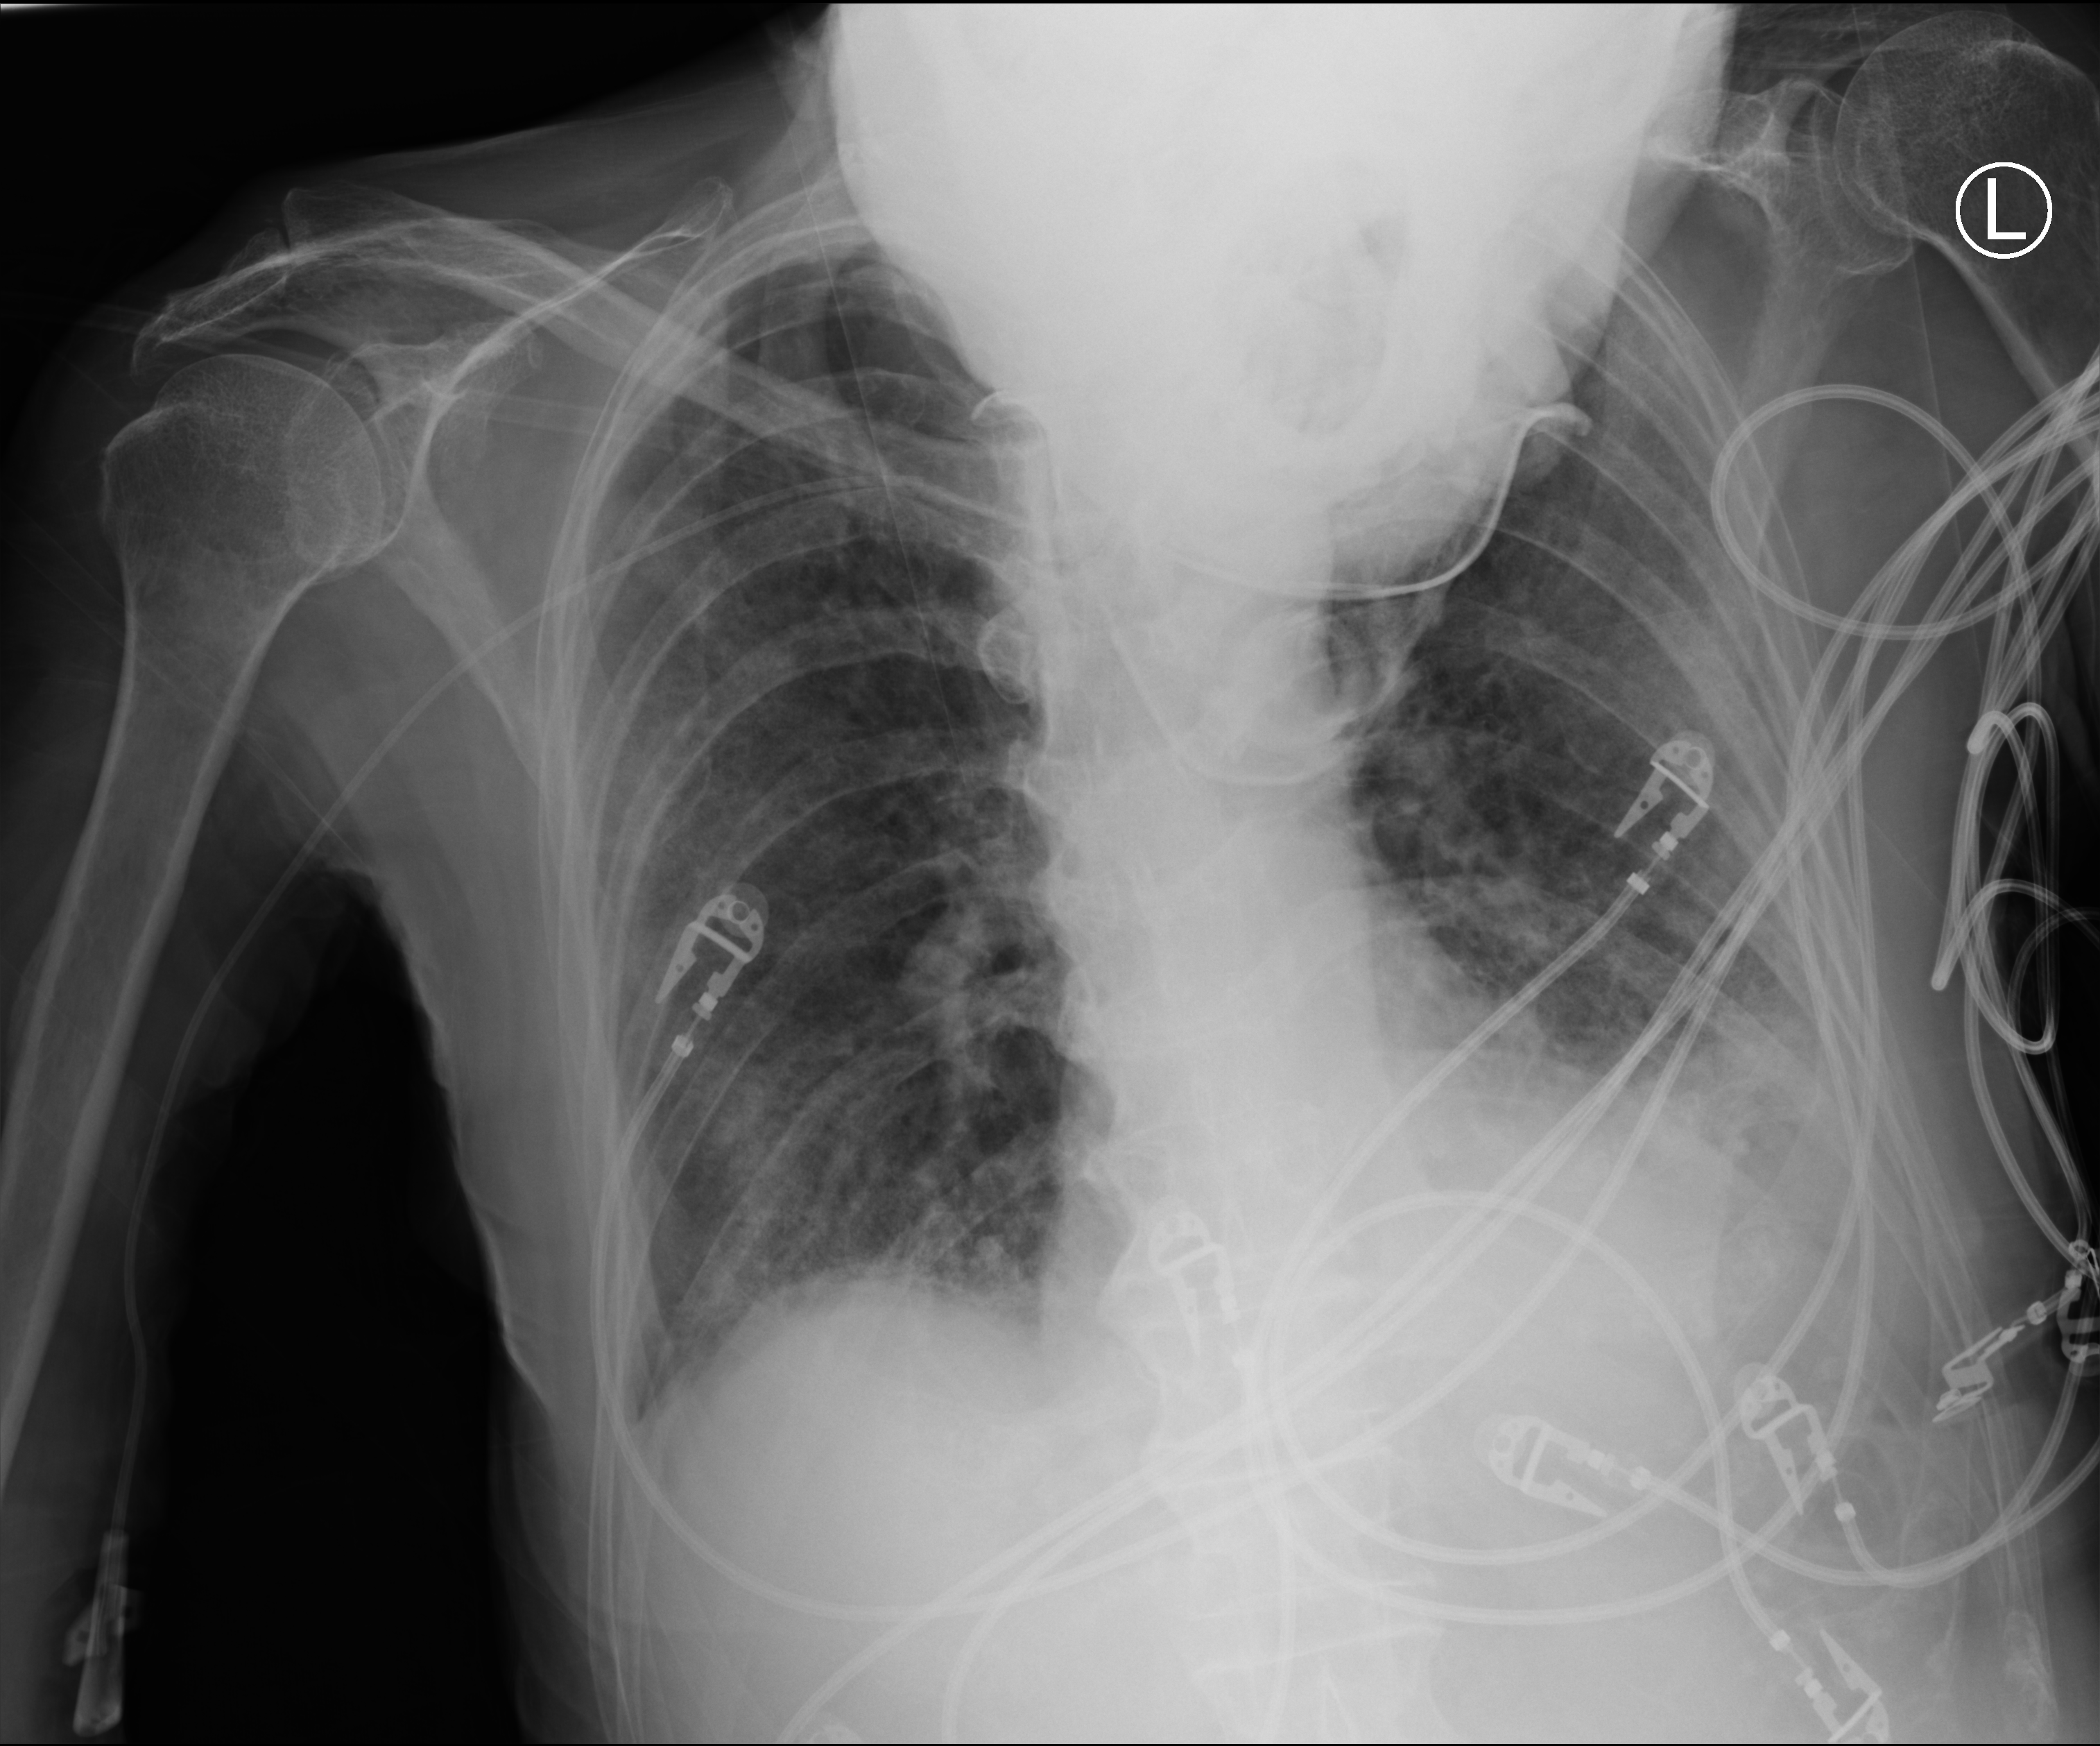
Portable chest radiograph, anteroposterior (AP) projection. Patient hospitalised with COVID-19; male, aged 60–74 years.
Hospital-stay facts (about this admission, not read from this image; timing relative to this image not recorded): hypertension (admission record): yes.